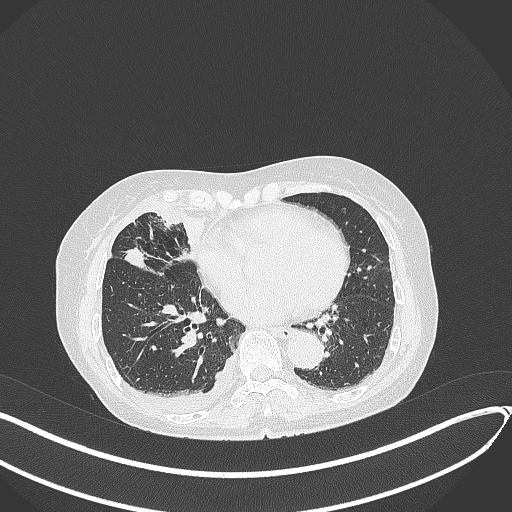
Chest CT, one axial slice; slice 156 of 418 in the series (ordered by position); reconstruction kernel B70f; lung window (W 1500 / L -600 HU); 1 mm slice thickness; 512 × 512 image matrix, field of view 400 × 400 mm. Female patient, age 75 years. Case-level facts recorded for this patient, not image findings: clinical TNM (as recorded): T2a N3 M0.
Annotated regions visible in this slice (bounding box drawn by a radiologist):
- lung tumour (recorded histology: adenocarcinoma): bounding box <122,244,151,271> (left, top, right, bottom; pixels)